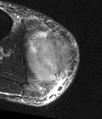
MRI of an extremity soft-tissue mass, one axial slice. Position 32 of 48 along the scan axis. T2-weighted fat-saturated. MR volume resampled by the dataset authors to the PET/CT grid (not the native acquisition matrix). 102 × 119 image matrix, field of view 100 × 116 mm. Male patient. Case-level facts recorded for this patient, not image findings: histological type: pleiomorphic liposarcoma; grade: high; site of the primary tumour: right calf.
Structures marked on this image (expert contour drawn on MRI and transferred to this co-registered scan by the dataset authors):
- gross tumour volume including surrounding oedema: bounding box (x1, y1, x2, y2) in pixels: (26, 30, 72, 84)
- gross tumour volume (mass): (30, 39, 72, 79)